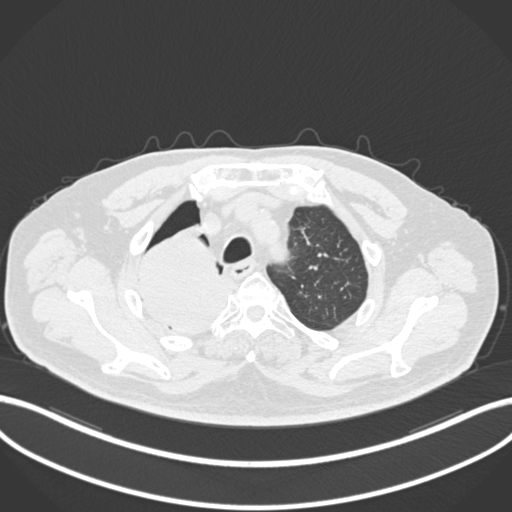
Chest CT, one axial slice. Position 173 of 218 along the scan axis. Reconstruction kernel B30f. 120 kVp. Lung window (W 1500 / L -600 HU). 512 × 512 image matrix, field of view 400 × 400 mm. Male patient, age 68 years. From the clinical record (not read from this slice): clinical TNM (as recorded): T2a N0 M0.
Structures marked on this image (bounding box drawn by a radiologist):
- lung tumour (recorded histology: adenocarcinoma): bounding box <130,218,236,339> (left, top, right, bottom; pixels)